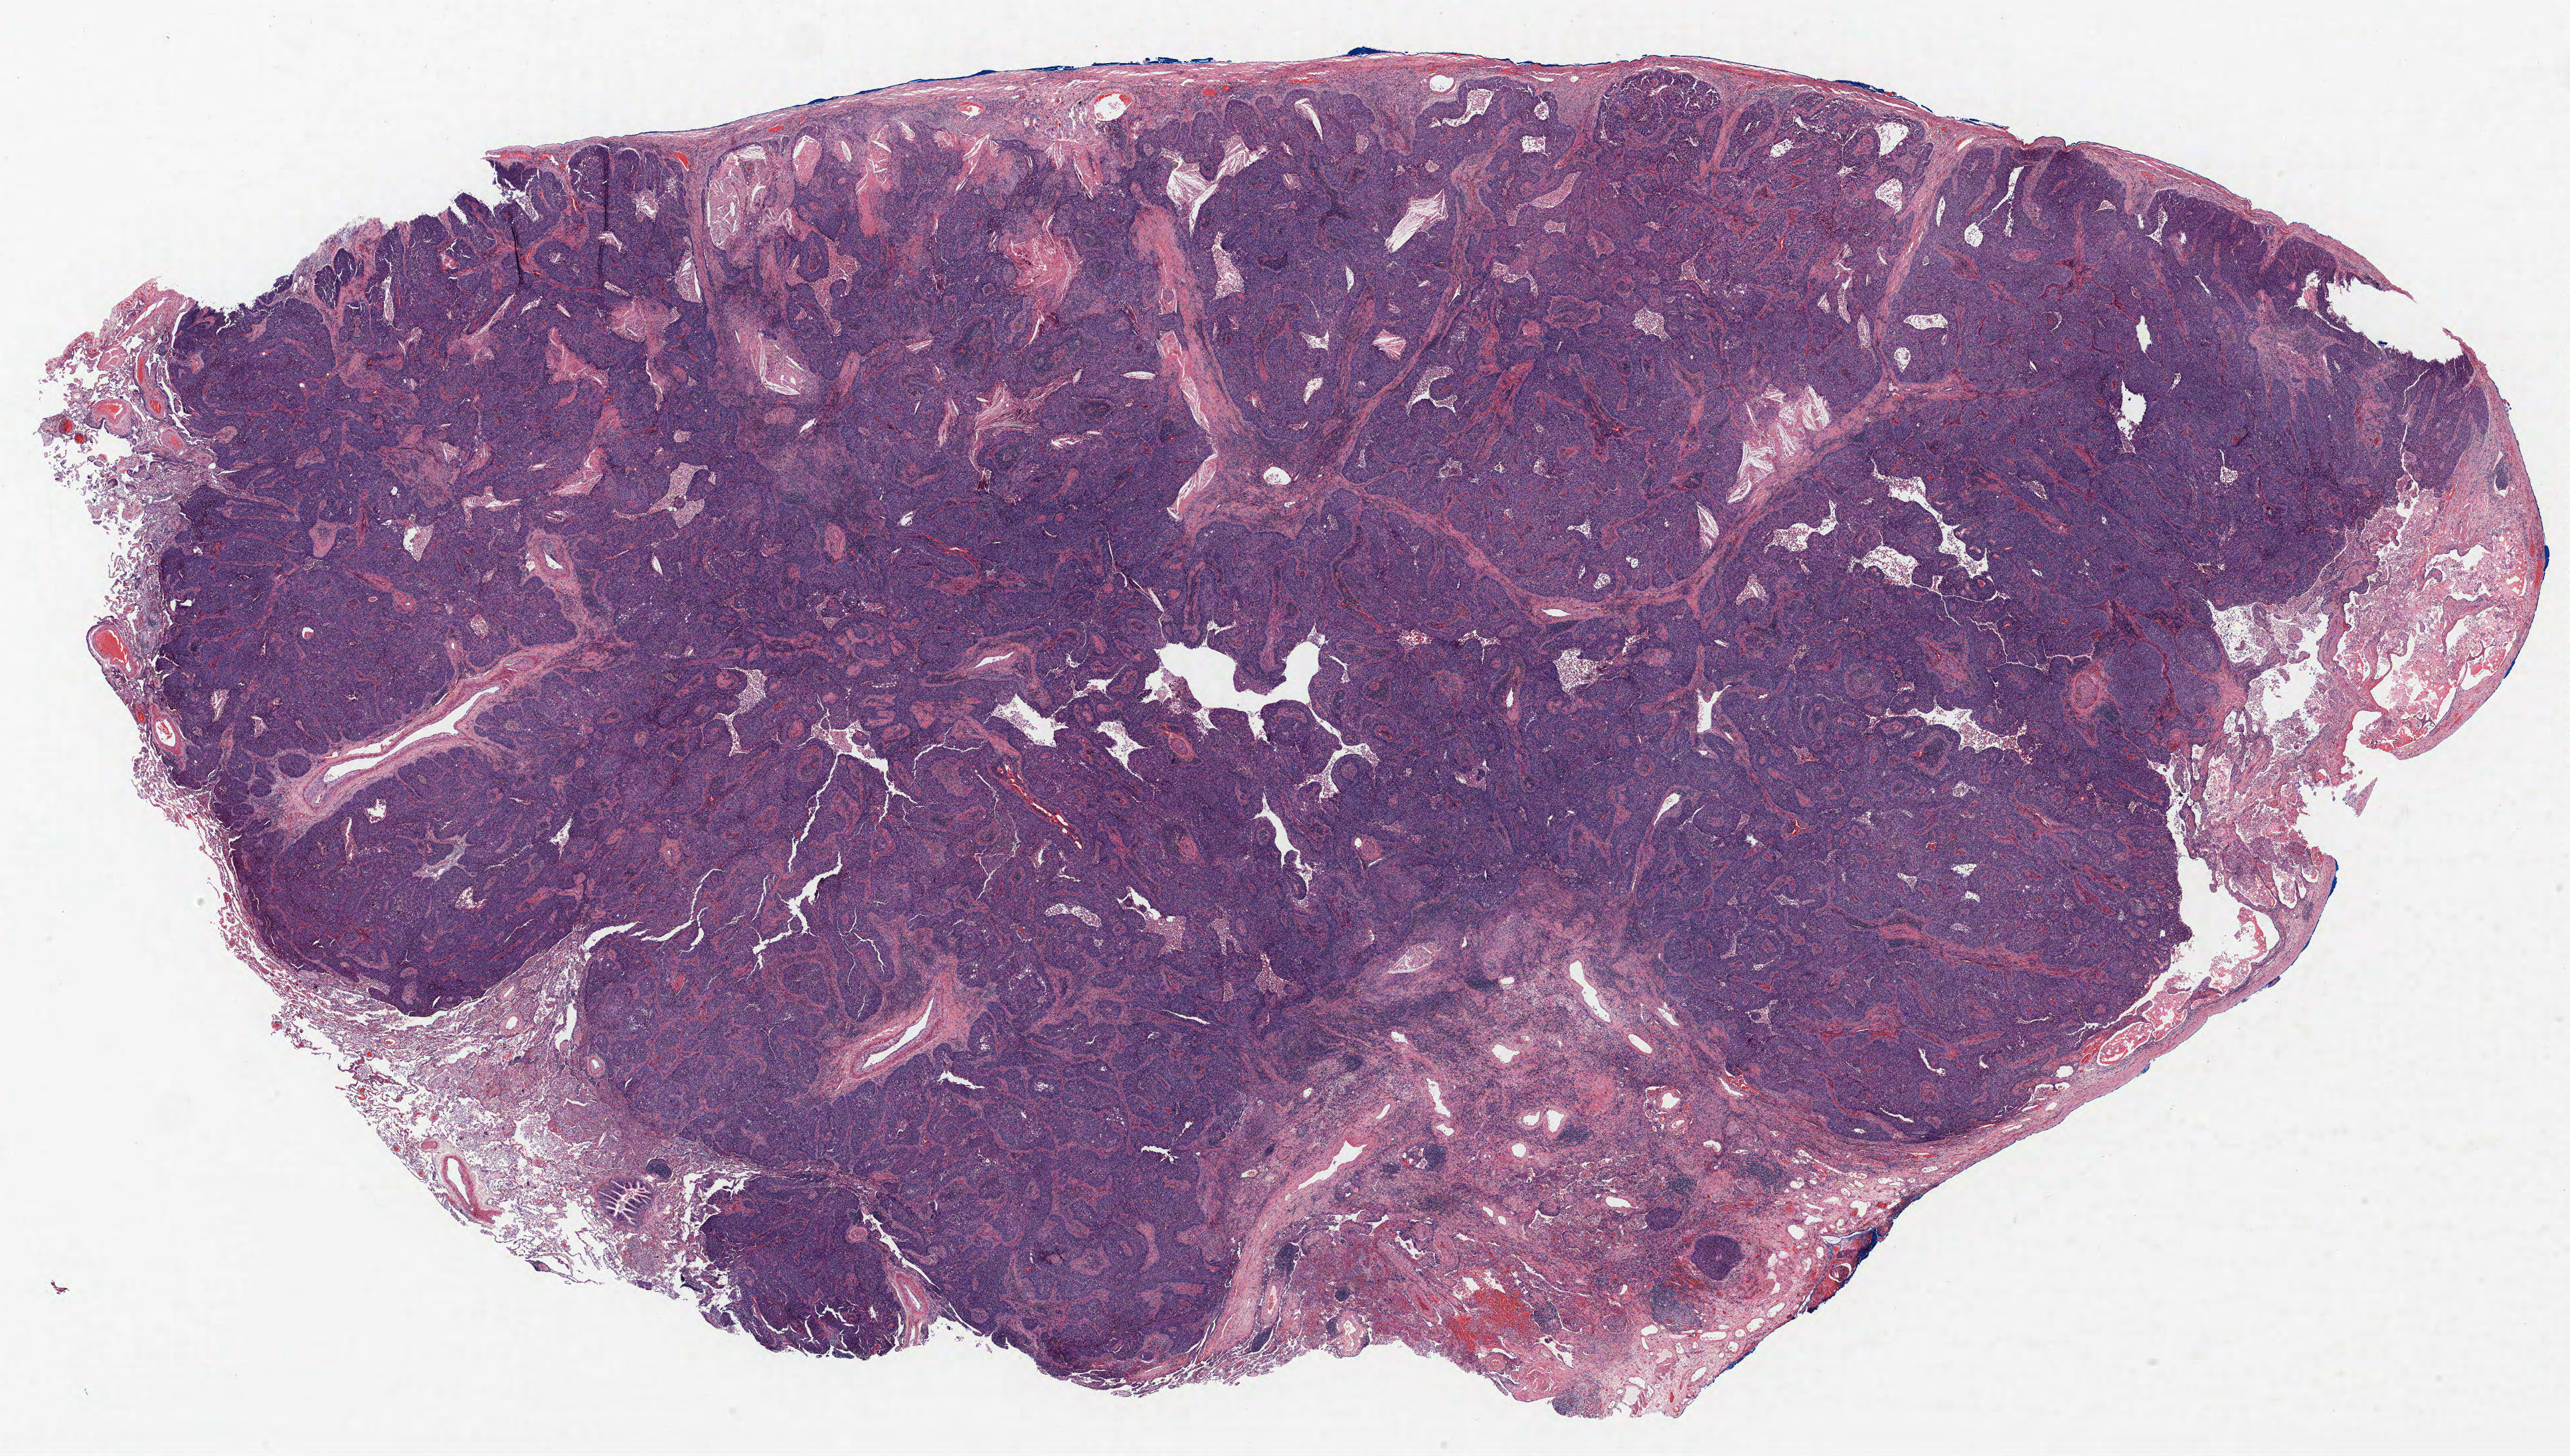
Hematoxylin and eosin (H&E) stained whole-slide image — low-resolution overview of the scanned area, about 31.0 x 17.5 mm (acquisition: 40x scan), formalin-fixed paraffin-embedded (FFPE) section, lung tissue. Male, age 68 at enrolment. Grade: poorly differentiated (G3).
Stage (AJCC 6th edition): IB. Participant's lung-cancer diagnosis: Squamous cell carcinoma, NOS (ICD-O-3 8070/3). Primary tumour location (clinical record): right lower lobe. Tumour size (pathology): 45 mm.